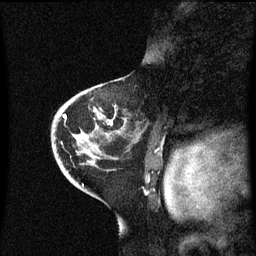
Breast MRI (dynamic contrast-enhanced), one sagittal slice; slice 38 of 60 in the series (ordered by position); dynamic contrast-enhanced series, image 2 of 3 at this slice position (ordered by acquisition); 1.5 T; TE 4.2 ms, TR 8.4 ms; 256 × 256 image matrix, field of view 200 × 200 mm. Patient: female, 46 years. Case-level facts recorded for this patient, not image findings: setting: breast cancer imaged before/during neoadjuvant chemotherapy; receptor status: HER2-positive.
Outlined on this slice (semi-automatic segmentation, software-assisted and operator-edited):
- analysis volume of interest (the breast-tissue region the enhancement analysis was run in; not a lesion): box from (x=52, y=86) to (x=137, y=171) px
- tumour enhancement mask (voxels above the 70 % enhancement threshold inside the analysis volume of interest): (x=64, y=110)–(x=97, y=139)